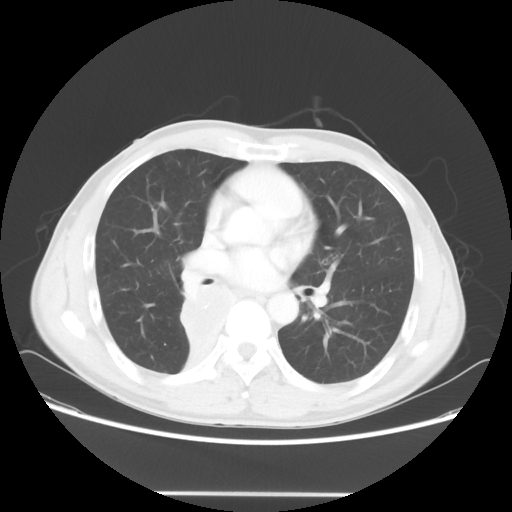
Chest CT, one axial slice; position 32 of 62 along the scan axis; 120 kVp; lung window (W 1500 / L -600 HU); 512 × 512 image matrix, field of view 393 × 393 mm. Male patient, age 47 years. Case-level facts recorded for this patient, not image findings: clinical TNM (as recorded): T2 N0 M0; histopathological grade: G2.
Outlined on this slice (bounding box drawn by a radiologist):
- lung tumour (recorded histology: squamous cell carcinoma): bounding box <172,270,231,348> (left, top, right, bottom; pixels)